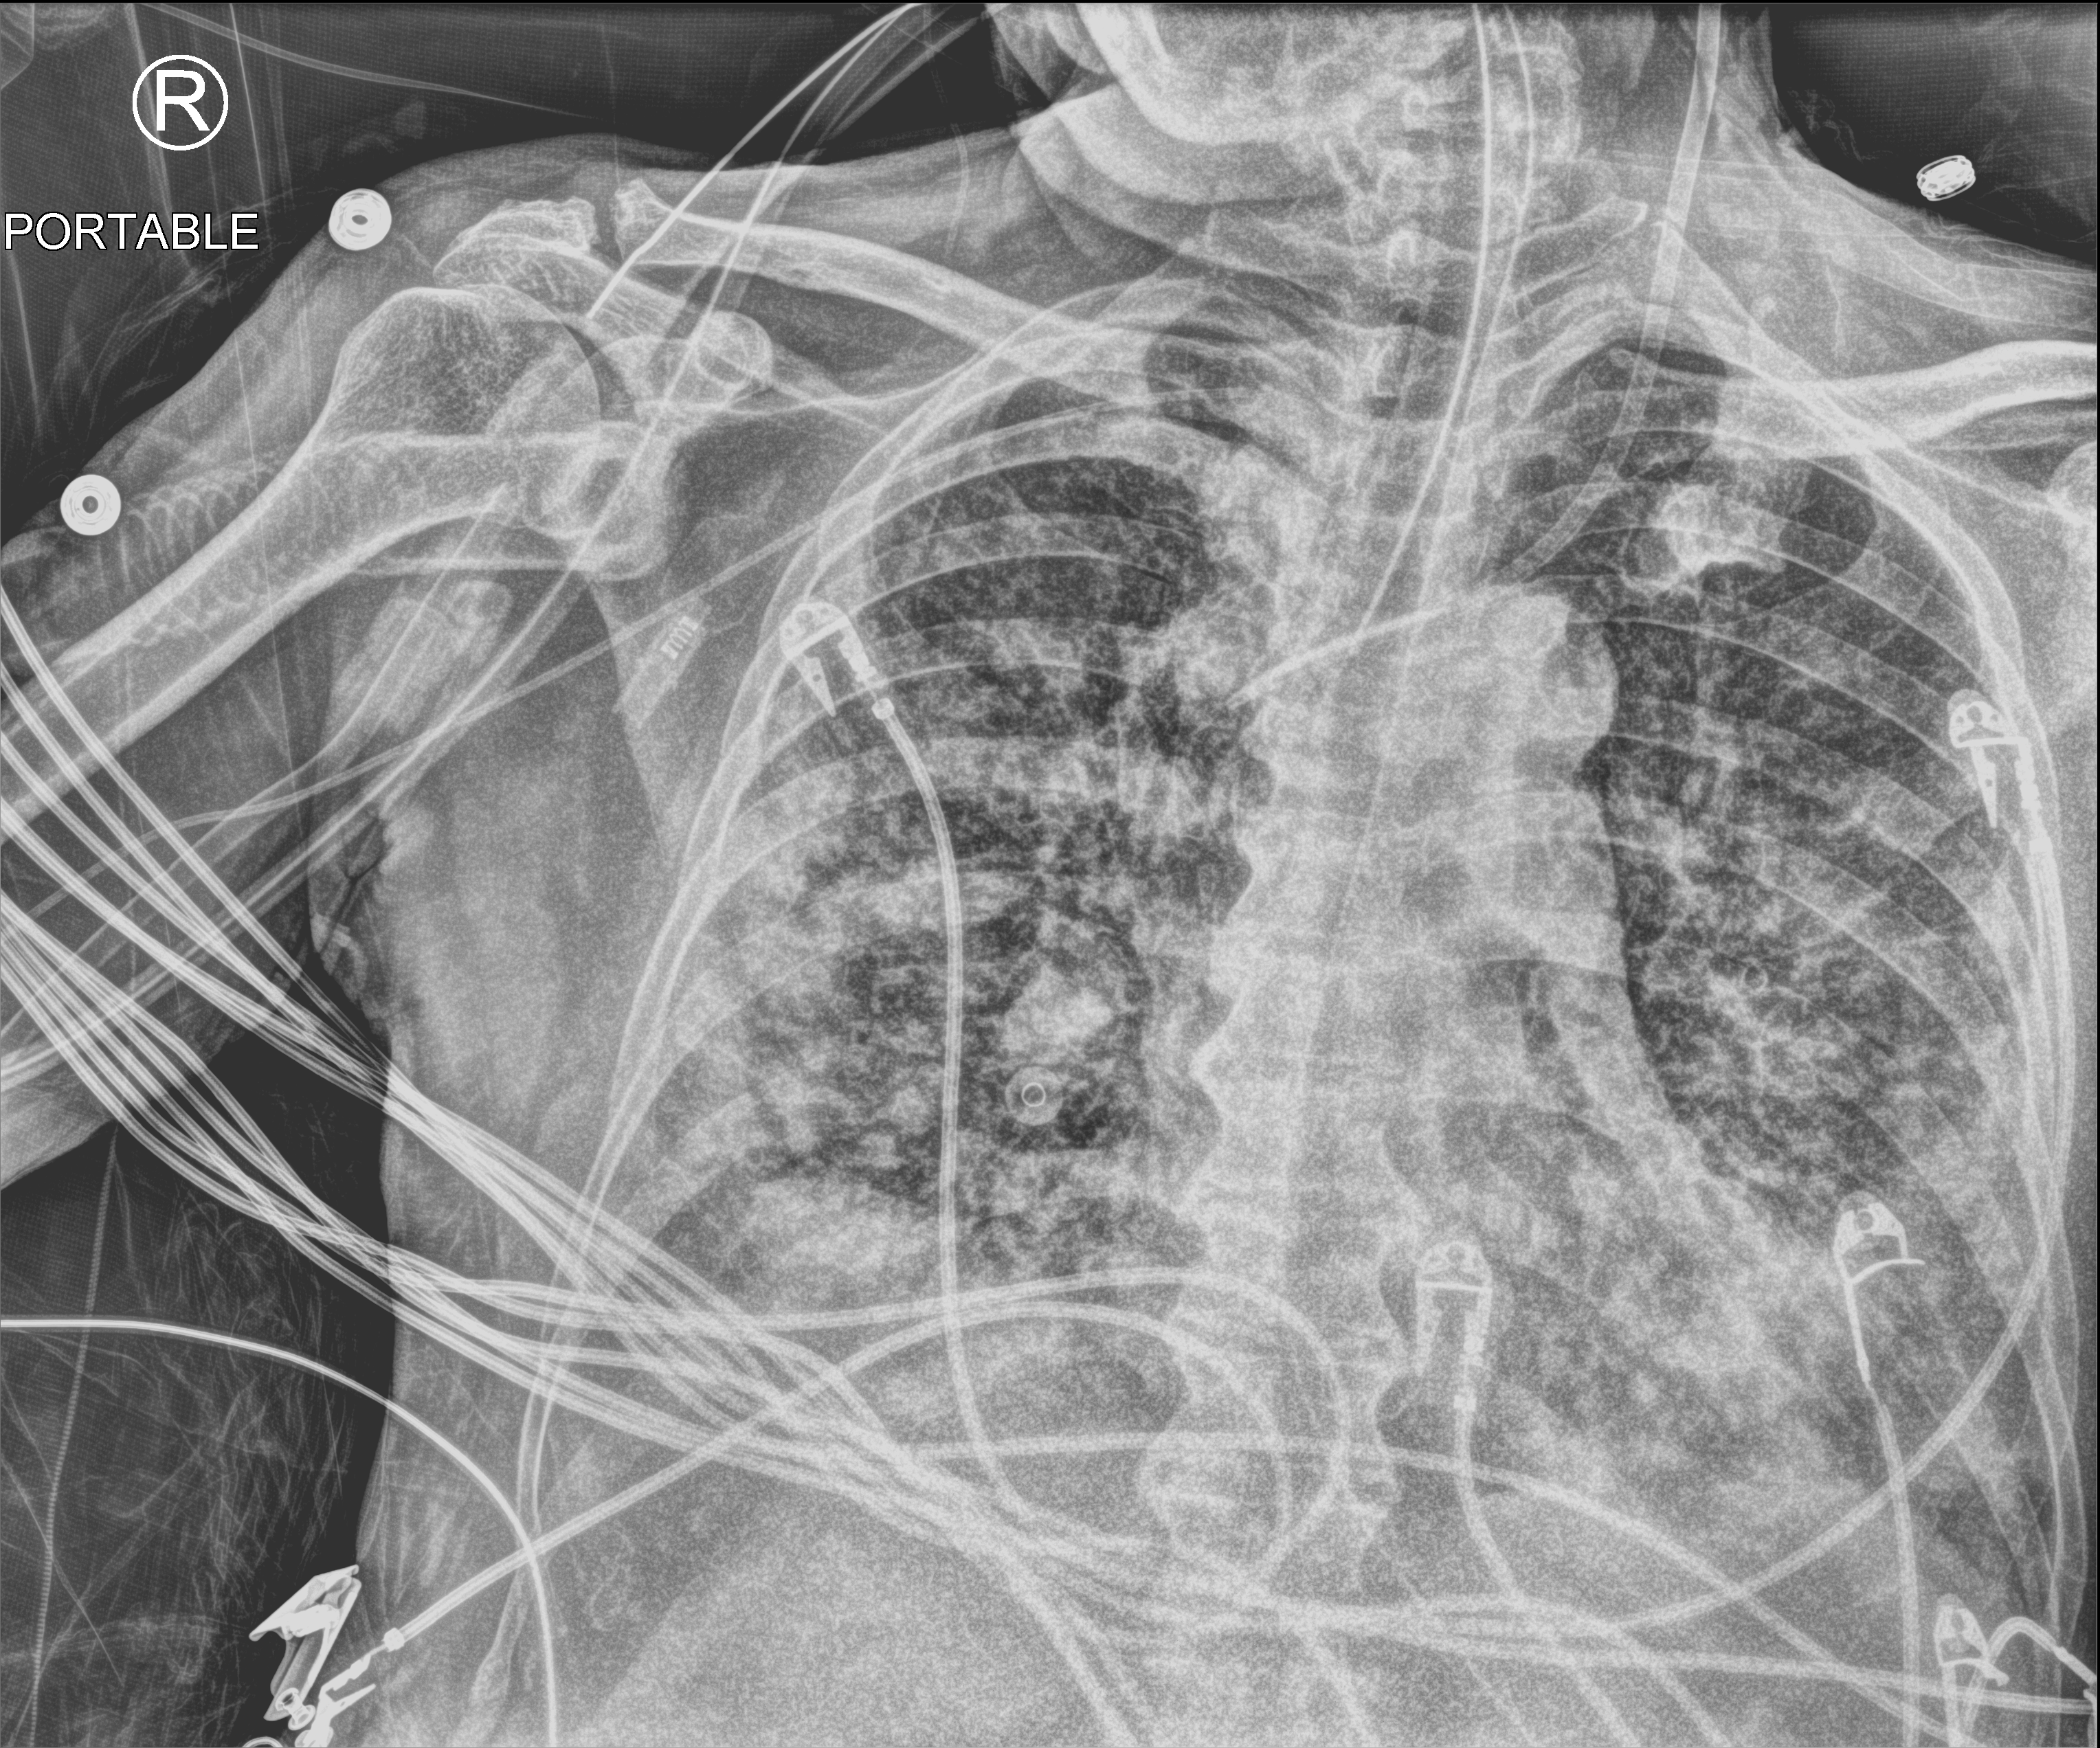
Portable chest radiograph, anteroposterior (AP) projection. Patient hospitalised with COVID-19; male, aged 60–74 years.
From the hospital-stay record, not from the radiograph (when in the stay this image was taken is not recorded):
- length of hospital stay: 26 days
- admitted to intensive care during this hospital stay: yes
- mechanically ventilated during this hospital stay: yes